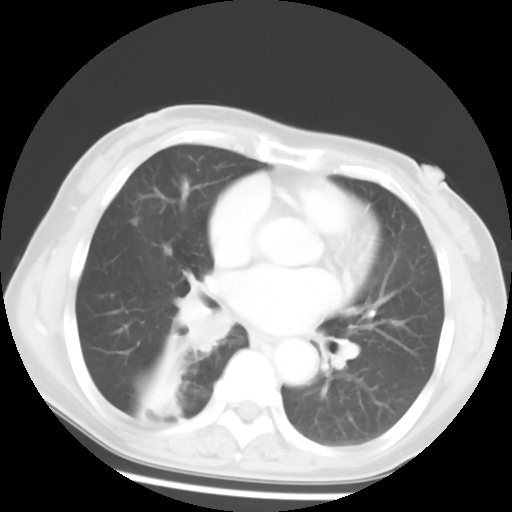
Chest CT, one axial slice; position 26 of 52 along the scan axis; reconstruction kernel STANDARD; 120 kVp; lung window (W 1500 / L -600 HU); 5 mm slice thickness; 512 × 512 image matrix, field of view 297 × 297 mm. Patient: female, 54 years. Case-level facts recorded for this patient, not image findings: clinical TNM (as recorded): T1c N0 M0; histopathological grade: G1-2.
Structures marked on this image (bounding box drawn by a radiologist):
- lung tumour (recorded histology: squamous cell carcinoma): bounding box [x1, y1, x2, y2] px = [169, 287, 239, 368]